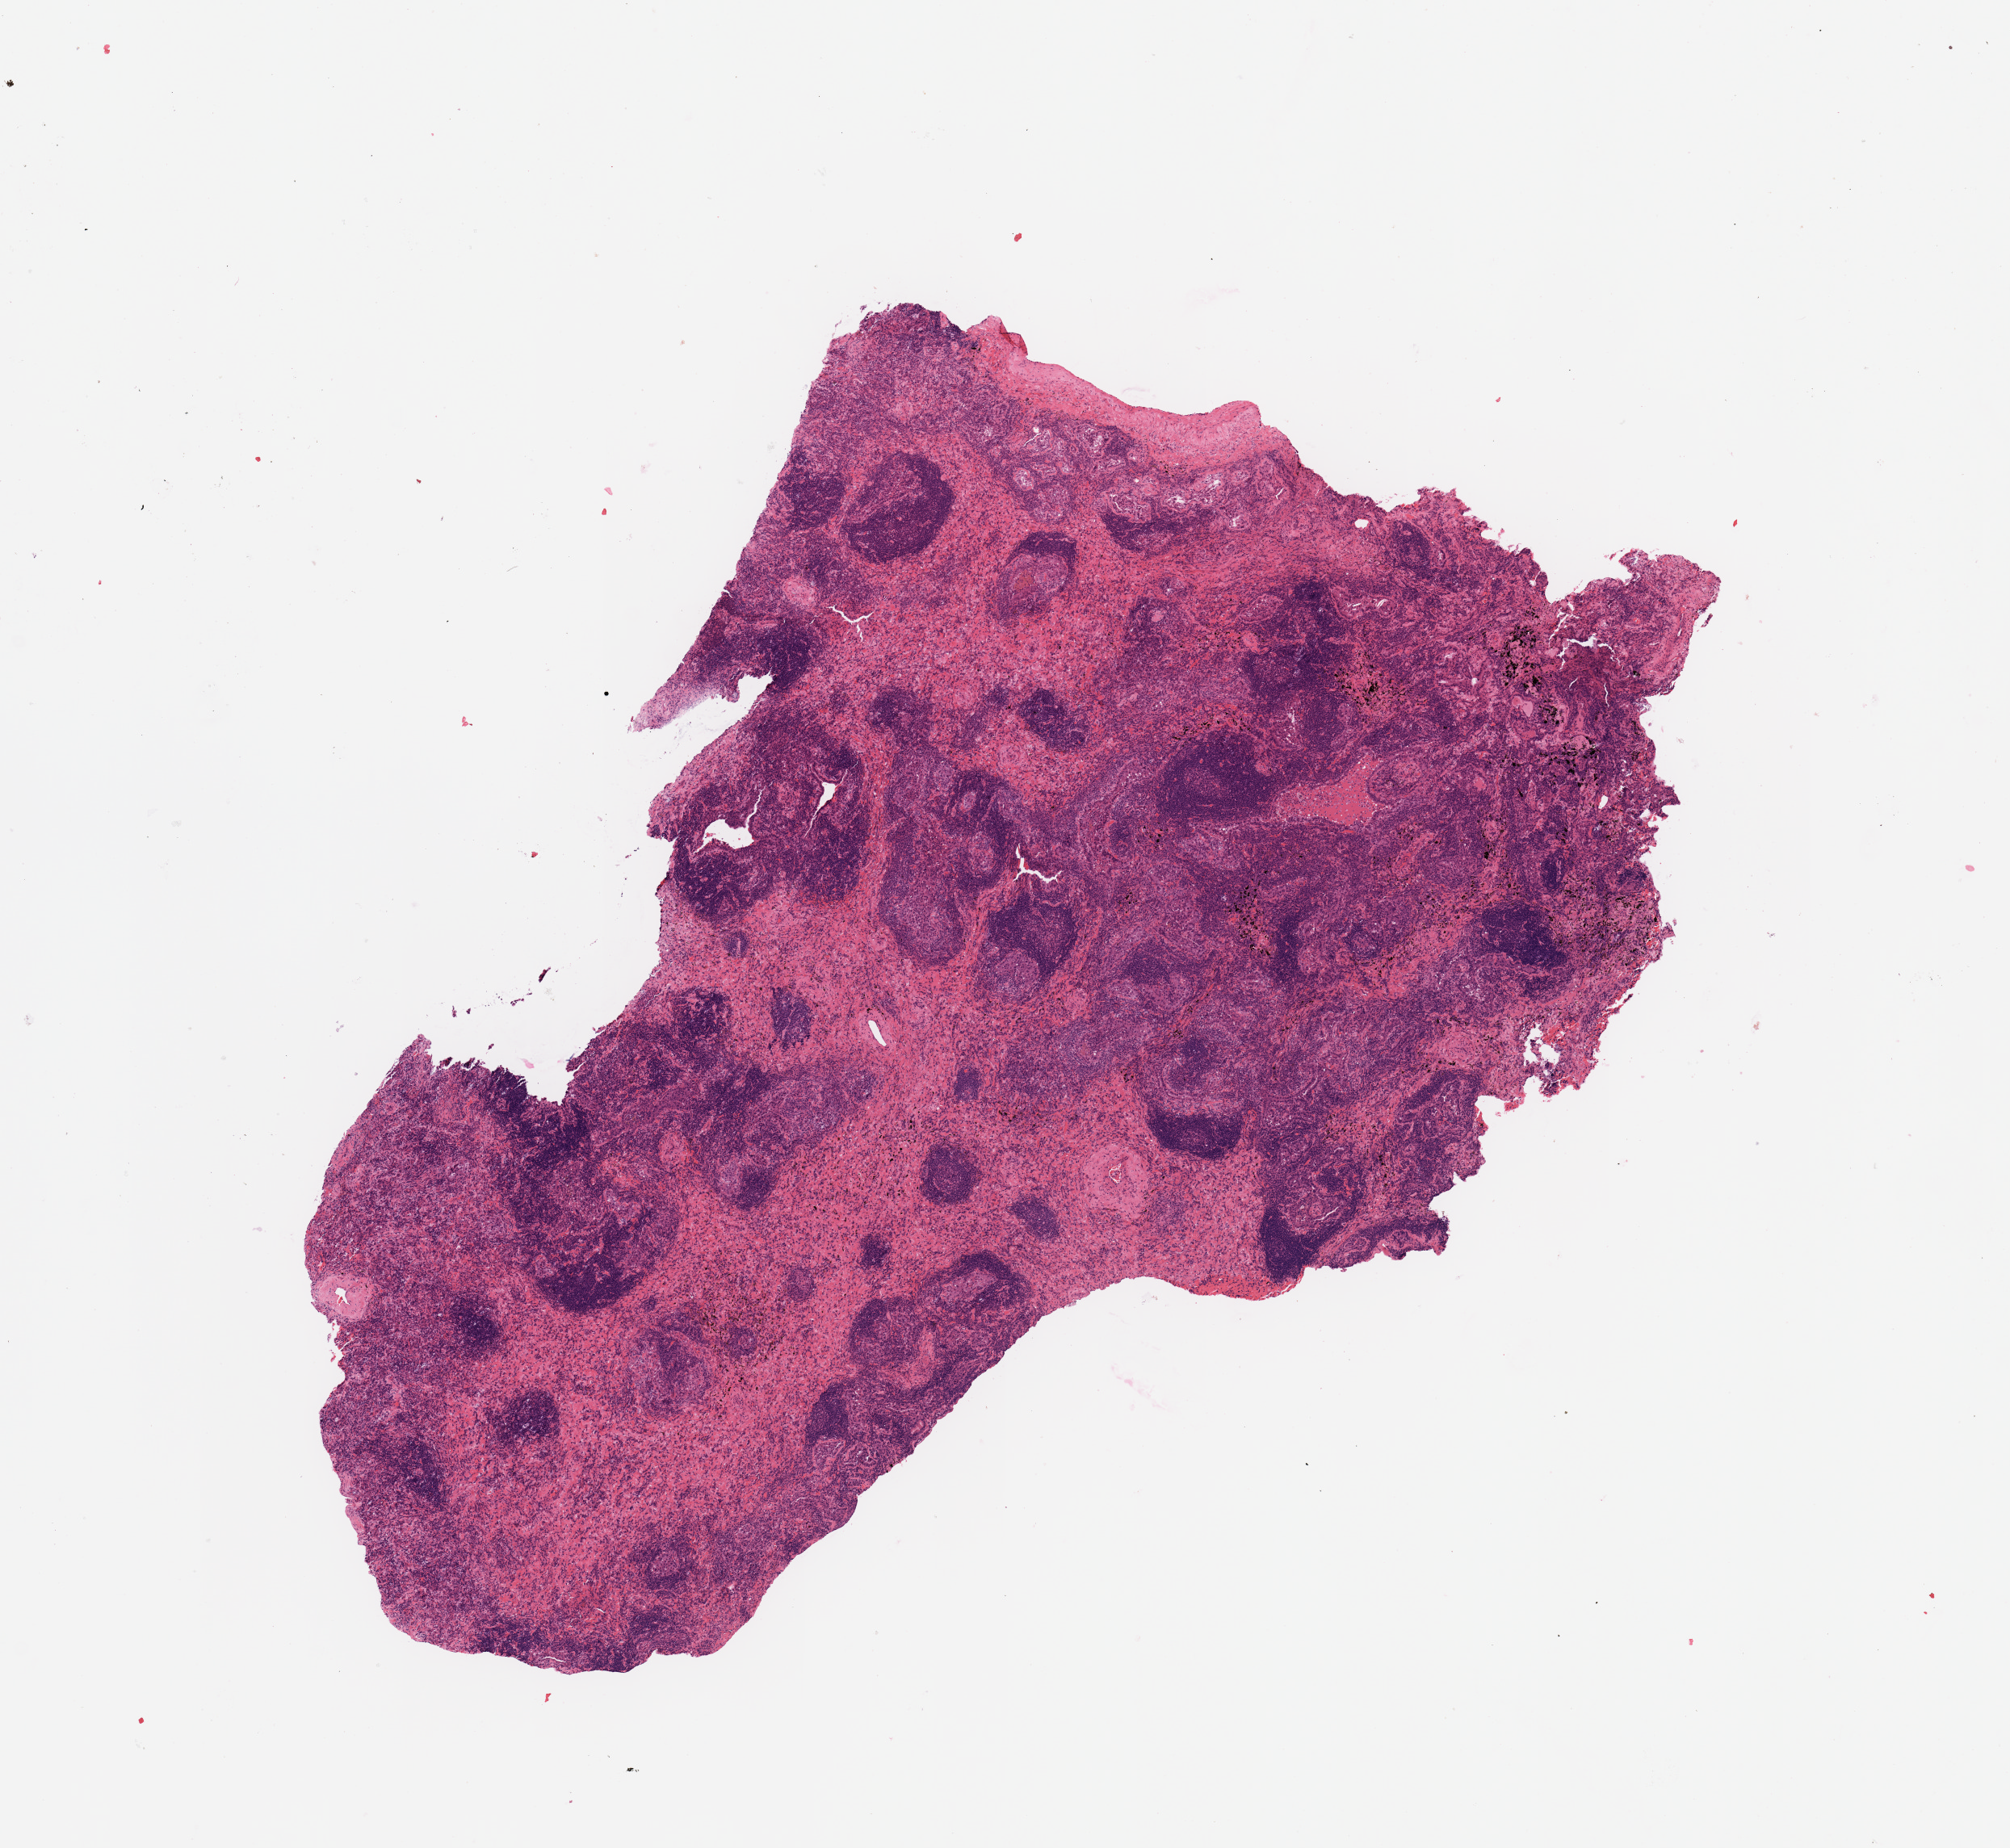
Hematoxylin and eosin (H&E) stained whole-slide image, whole scanned area (about 9.8 x 9.1 mm) shown as a low-resolution overview, tumour tissue sample, sampled site: lung. Patient: male, age 68 years. Histologic grade: G2 (moderately differentiated). Pathologist review of this section (percent, as recorded): tumour nuclei 50%, necrosis 0%.
Diagnosis: Adenocarcinoma, NOS. Primary tumour site (as recorded): right upper lobe. AJCC pathologic stage: IA2.